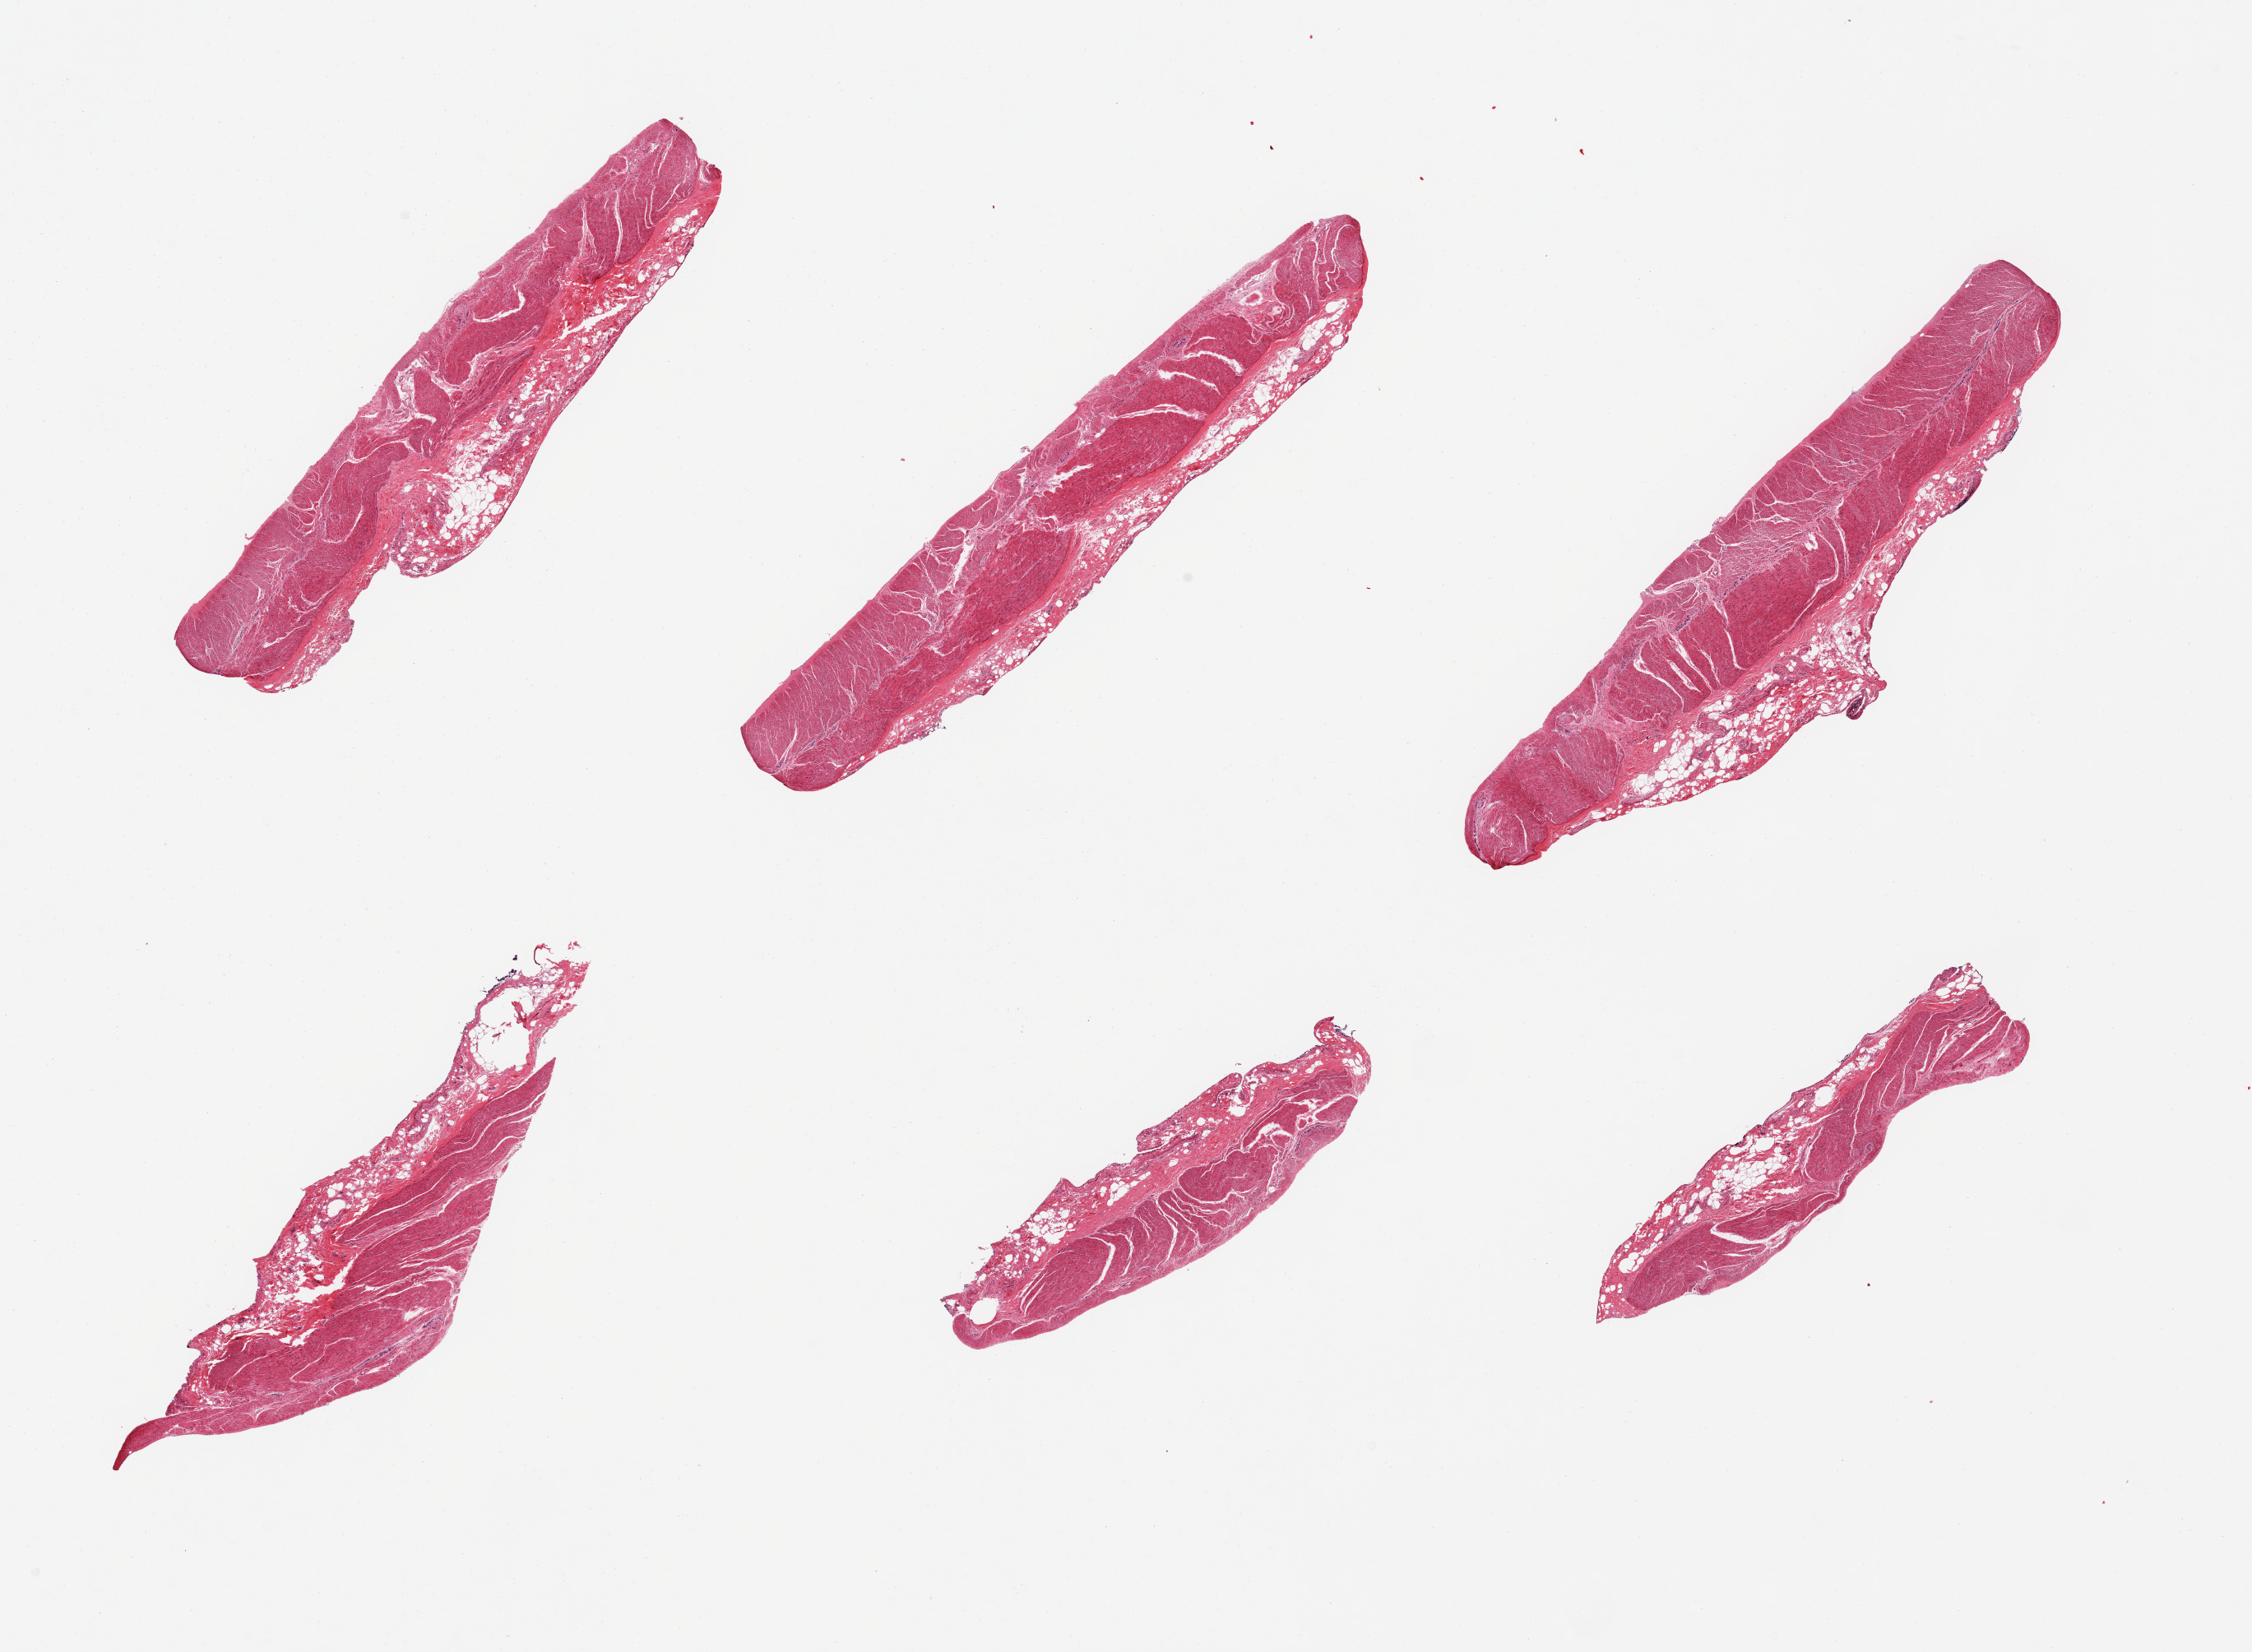
H&E whole-slide image, low-resolution overview of the scanned area, about 21.7 x 15.9 mm. PAXgene-fixed paraffin-embedded (PFPE) section. Target tissue: sigmoid colon. Tissue donor sample. Donor: female.
Review note (as recorded): 6 pieces; up to 0.9 mm submucosal fat.